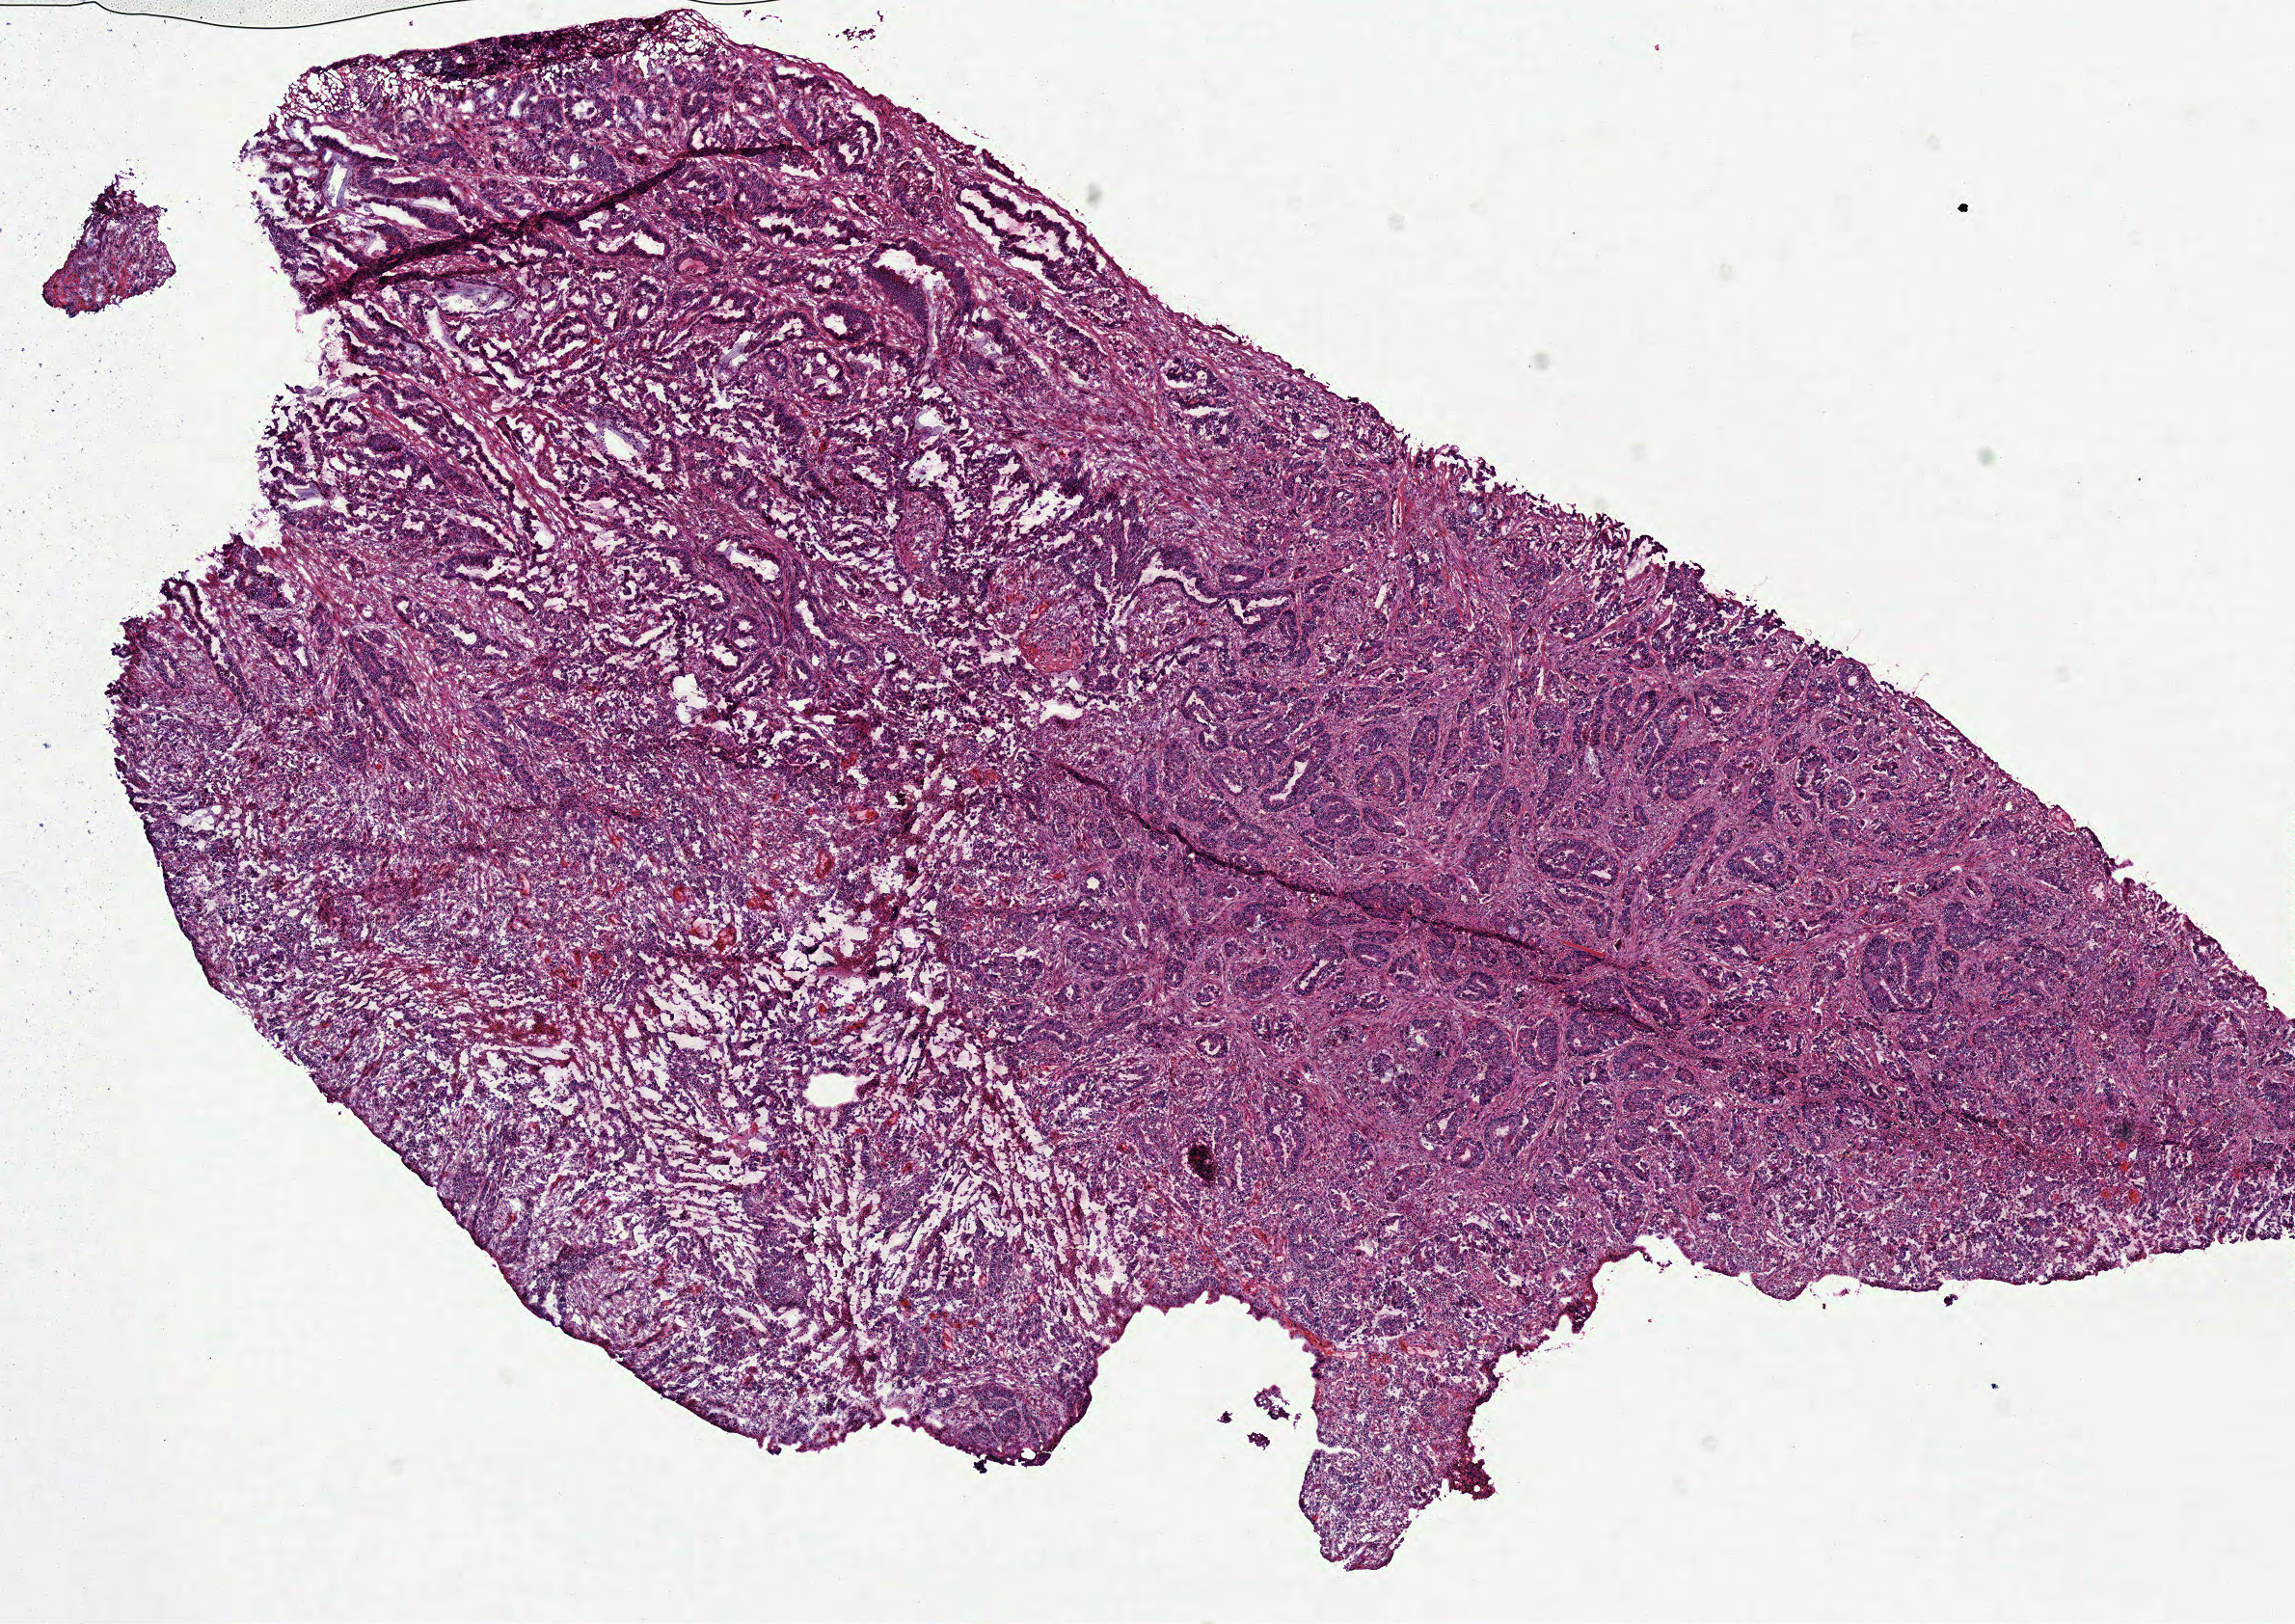
Whole-slide histology image, H&E-stained — a low-resolution overview of the entire scanned area, about 9.4 x 6.6 mm (acquisition: 40x scan); frozen section; primary tumour sample from the colon. Female, age 45 years at initial diagnosis. Slide review estimates, as recorded: tumour cells 90%, tumour nuclei 80%, normal cells 0%, stromal cells 10%, necrosis 0%.
Histologic diagnosis: Adenocarcinoma, NOS. AJCC pathologic stage: III. Lymph nodes positive (case pathology): 3 of 20 examined. TNM: T3 N1 M0.